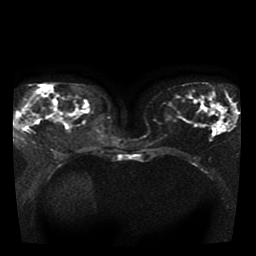
Breast MRI, one axial slice; slice 17 of 41 in the series (ordered by position); diffusion-weighted series; image 2 of 4 stored at this slice position (different b-values; order by instance number); 1.5 T; 256 × 256 image matrix, field of view 330 × 330 mm. Female patient.
Outlined on this slice (outlined manually by an expert reader):
- tumour on diffusion-weighted imaging: box from (x=22, y=118) to (x=35, y=127) px